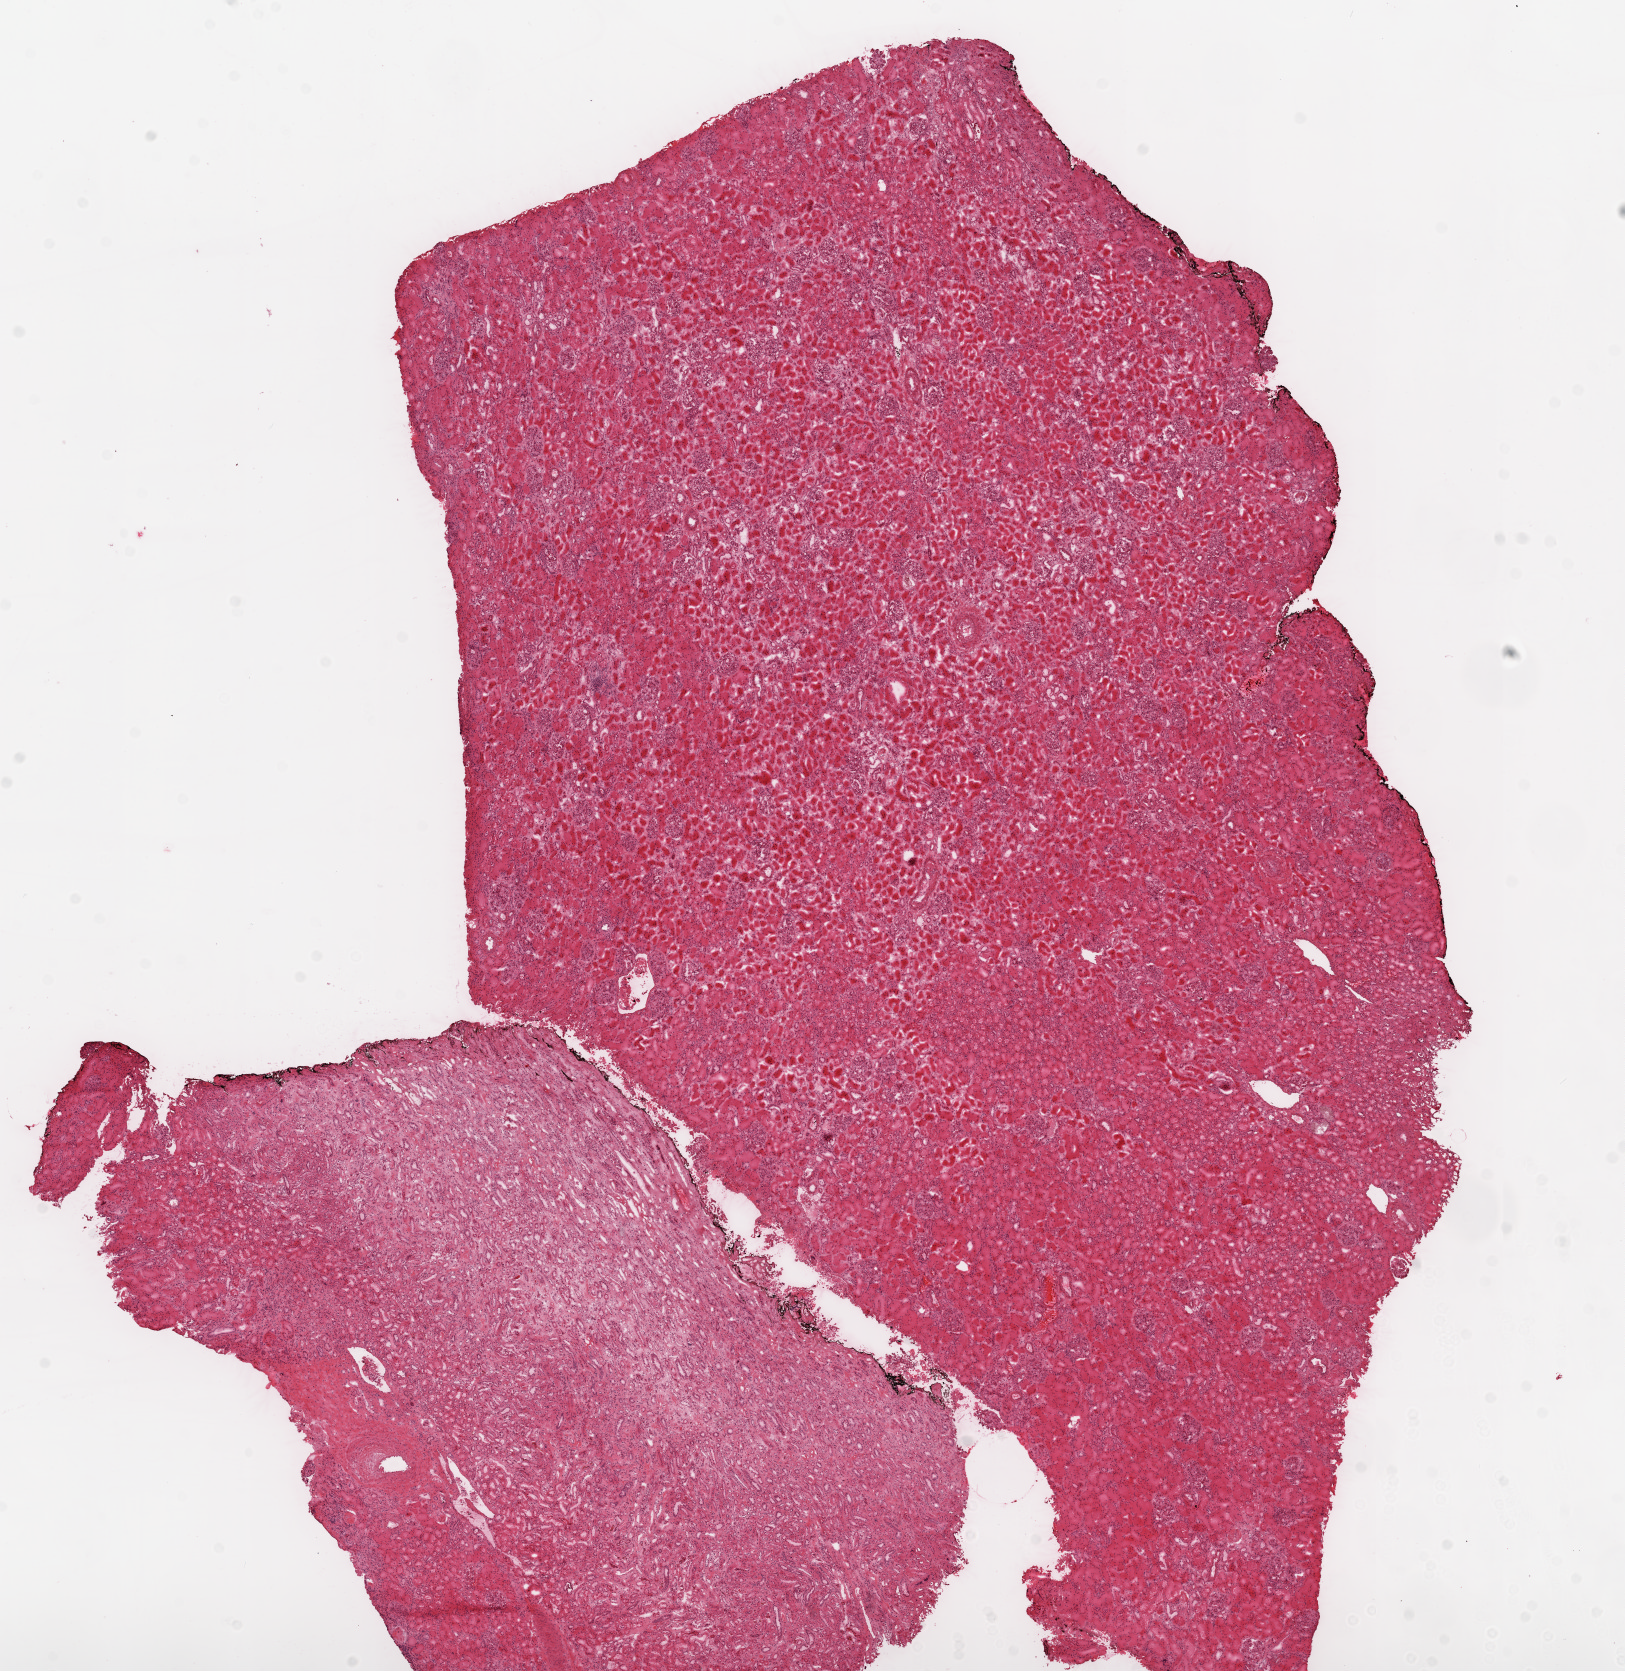
Digitized H&E tissue section (whole slide), whole scanned area (about 13.0 x 13.4 mm, acquisition: 20x scan) shown as a low-resolution overview. Frozen section from the top of the tissue portion. Sample: solid tissue normal (non-tumour tissue), kidney. Male, age 54 years at initial diagnosis.
- this section: solid tissue normal sample (biorepository sample class)
- patient diagnosis: Clear cell adenocarcinoma, NOS